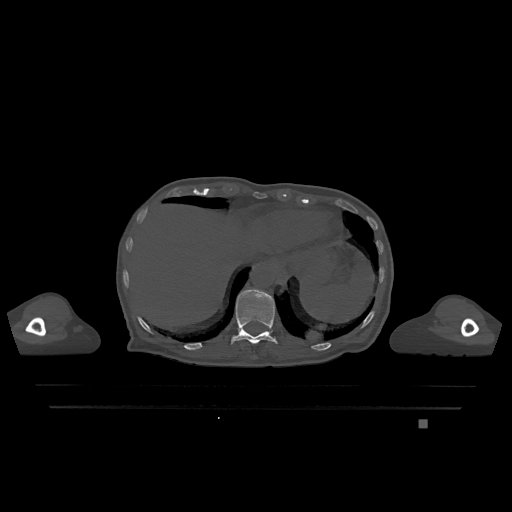
CT including the spine, one axial slice. Position 588 of 1317 along the scan axis. Bone window (W 1800 / L 400 HU). 0.5 mm slice thickness. 512 × 512 image matrix, field of view 500 × 500 mm. Female patient, age 74 years. Case-level facts recorded for this patient, not image findings: primary cancer: lung; vertebrae with lytic lesions (as recorded): T1, T4, T5, T6, L4, L5.
Outlined on this slice (semi-automatically segmented with operator editing):
- T11 vertebra: bounding box (x1, y1, x2, y2) in pixels: (231, 289, 278, 345)